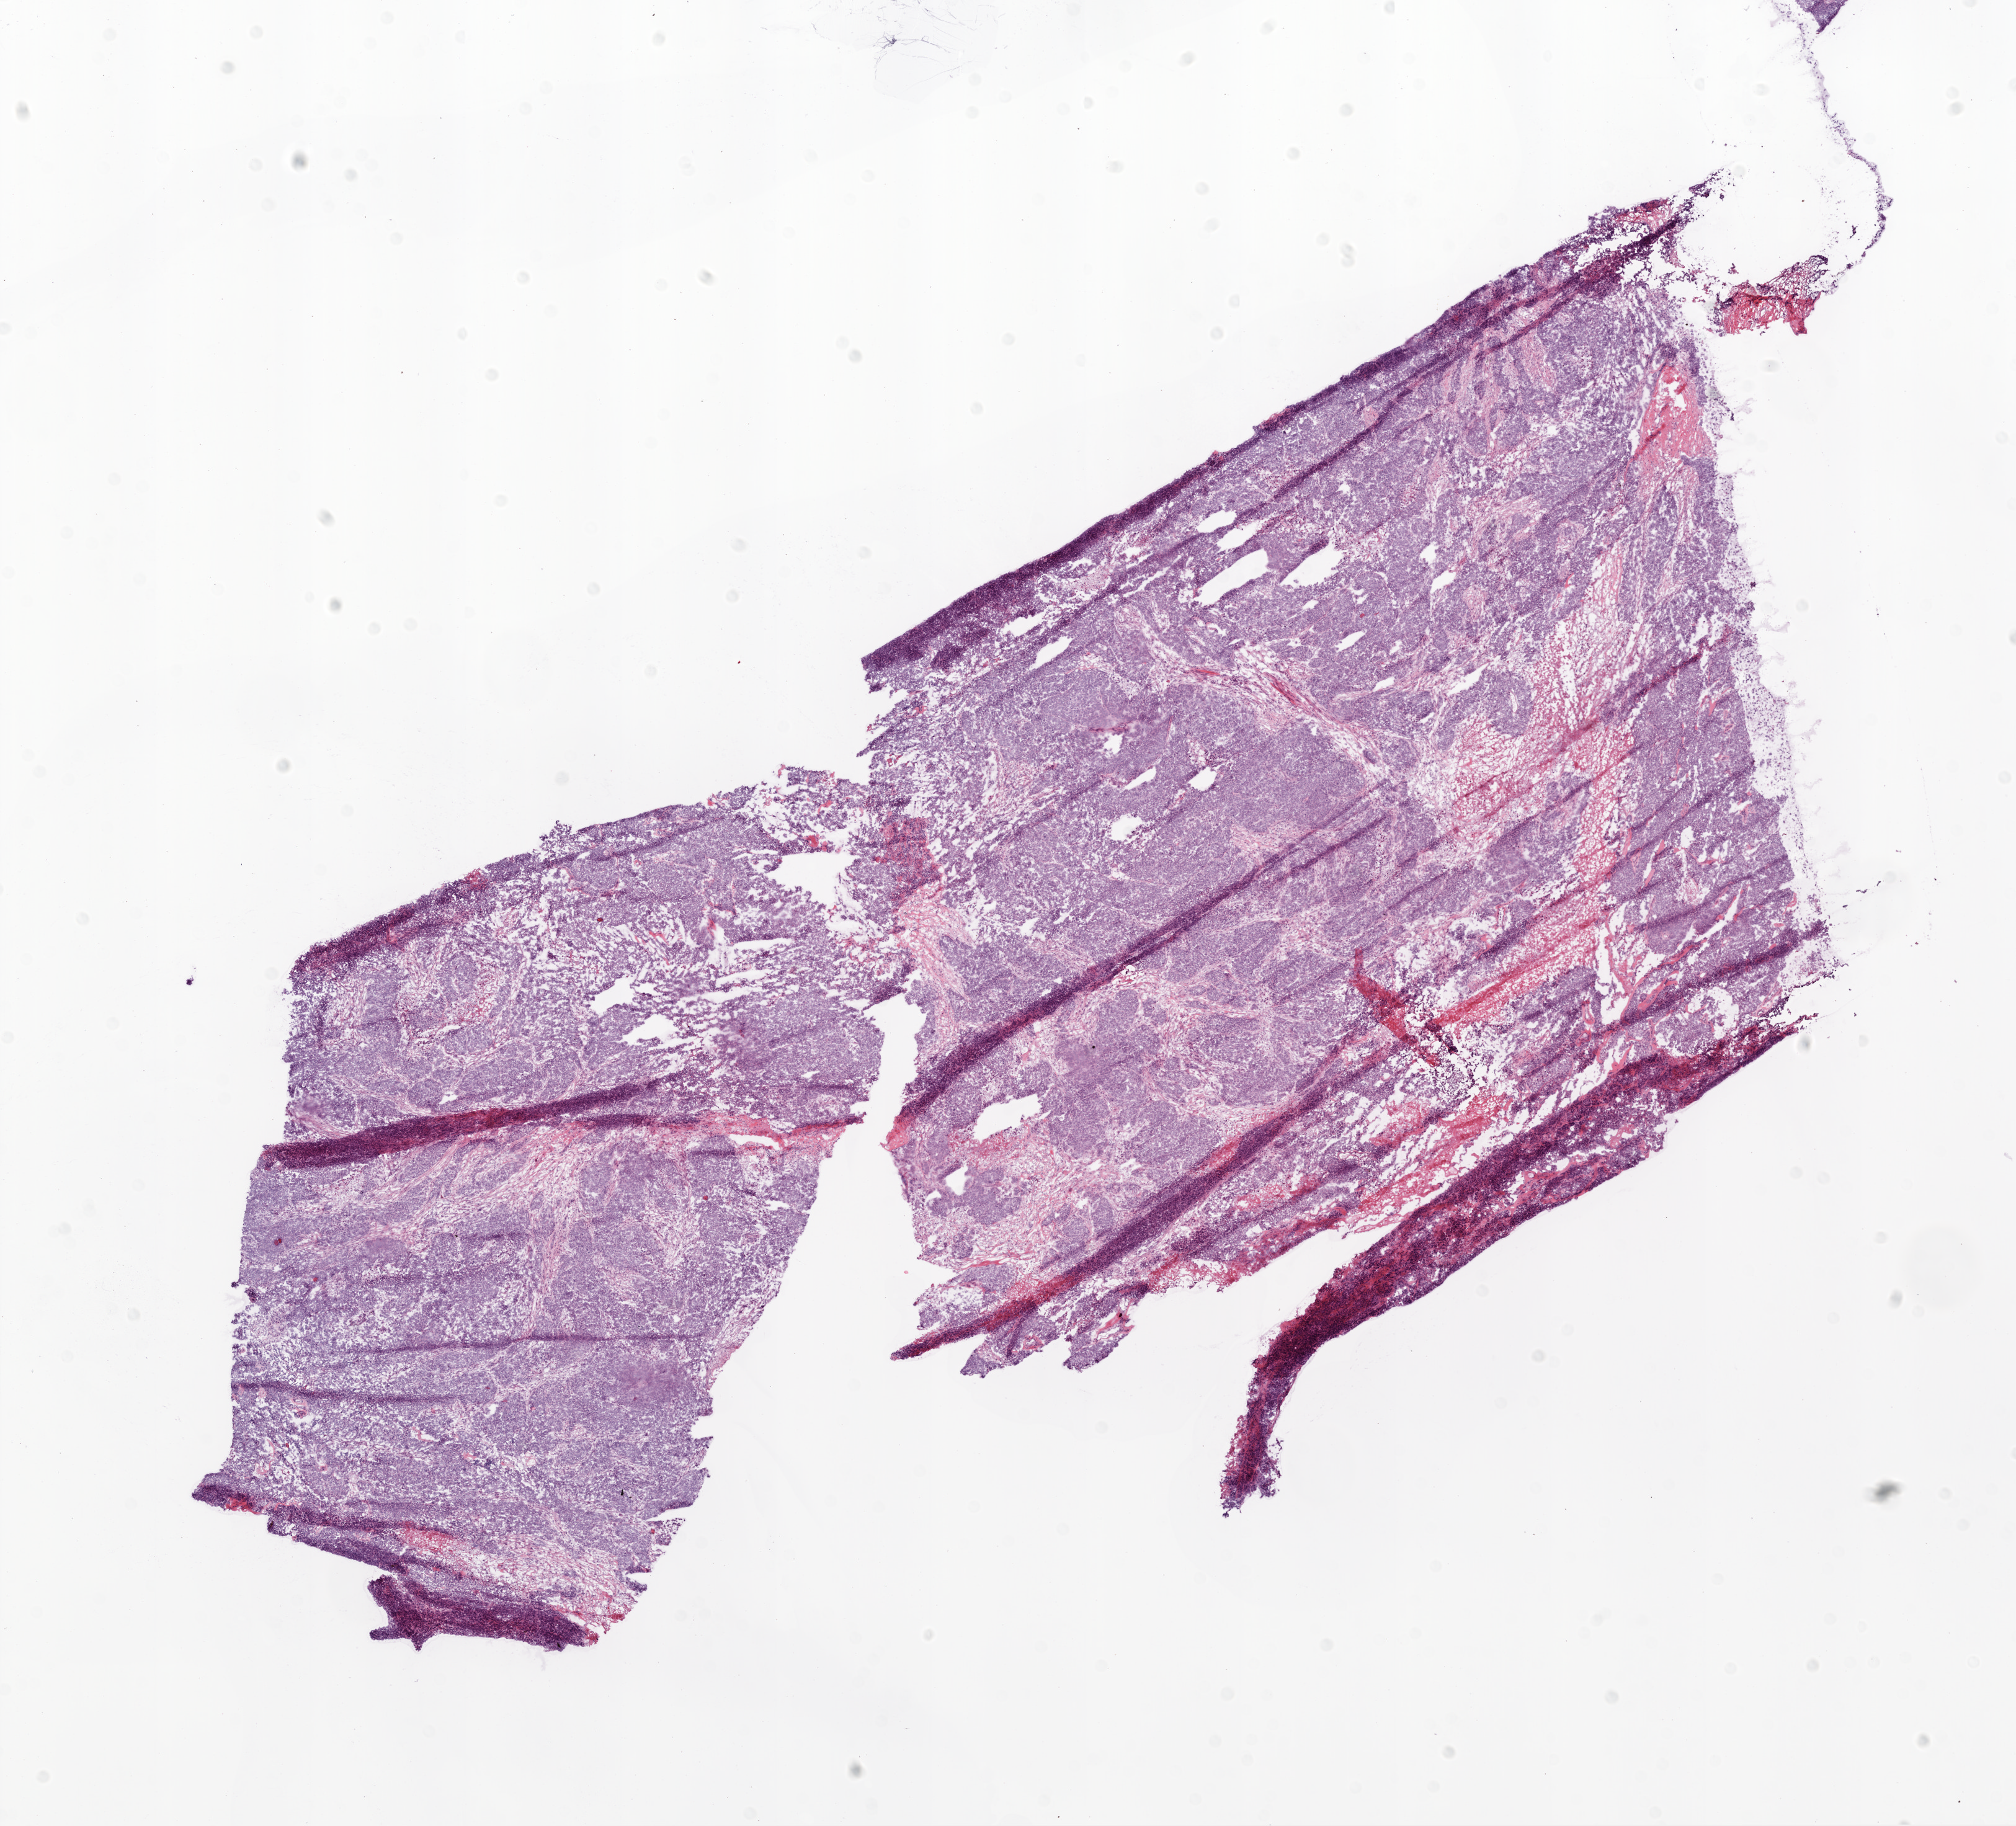
Digitized Hematoxylin and eosin (H&E) stained tissue section (whole slide), shown as a low-resolution overview of the whole scanned area (about 13.0 x 11.8 mm), frozen section, primary tumour sample from the ovary. Female, age 67 years at initial diagnosis. Histologic grade: G3 (poorly differentiated). Slide review estimates, as recorded: tumour cells 65%, tumour nuclei 90%, normal cells 10%, stromal cells 10%, necrosis 15%.
Diagnosis: Serous cystadenocarcinoma, NOS. Laterality: bilateral. FIGO stage: IIIC.